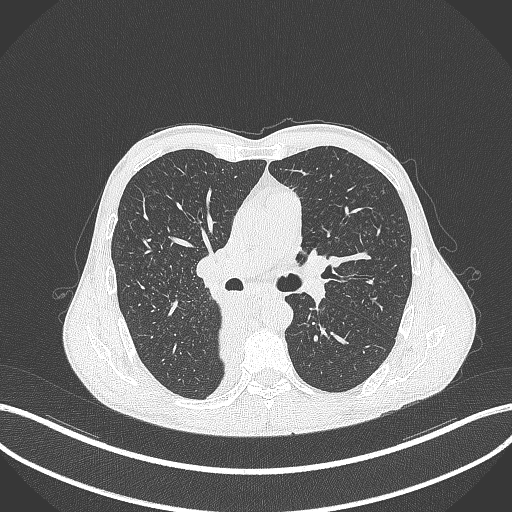
Chest CT, one axial slice. Slice 224 of 371 in the series (ordered by position). 120 kVp. Lung window (W 1500 / L -600 HU). 512 × 512 image matrix, field of view 400 × 400 mm. Patient: male, 58 years. Case-level facts recorded for this patient, not image findings: clinical TNM (as recorded): T3 N1 M1.
Outlined on this slice (bounding box drawn by a radiologist):
- lung tumour (recorded histology: squamous cell carcinoma): bounding box (x1, y1, x2, y2) in pixels: (210, 308, 247, 373)